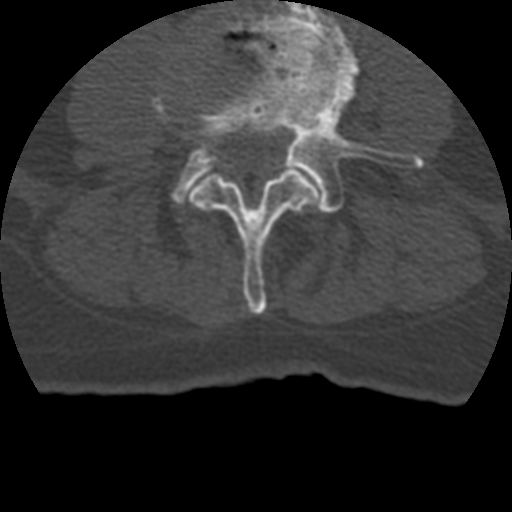
CT including the spine, one axial slice; slice 77 of 399 in the series (ordered by position); reconstruction kernel STANDARD; bone window (W 1800 / L 400 HU); 1.25 mm slice thickness; 512 × 512 image matrix, field of view 160 × 160 mm. Patient age 69 years. Case-level facts recorded for this patient, not image findings: primary cancer: prostate.
Structures marked on this image (semi-automatic segmentation, software-assisted and operator-edited):
- L3 vertebra: box from (x=156, y=94) to (x=318, y=314) px
- L4 vertebra: (x=172, y=0)–(x=425, y=213)